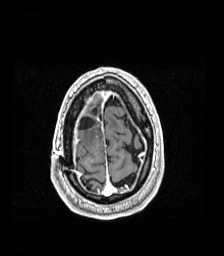
Brain MRI from a brain-tumour surgery series, one axial slice. Slice 31 of 192 in the series (ordered by position). T1-weighted post-contrast. 224 × 256 image matrix, field of view 224 × 256 mm. From the clinical record (not read from this slice): histopathology: Astrocytoma; WHO grade: 4; IDH mutation: yes; tumour location: Right Frontal.
Outlined on this slice (expert manual segmentation):
- previous resection cavity: bounding box (x1, y1, x2, y2) in pixels: (79, 117, 95, 131)